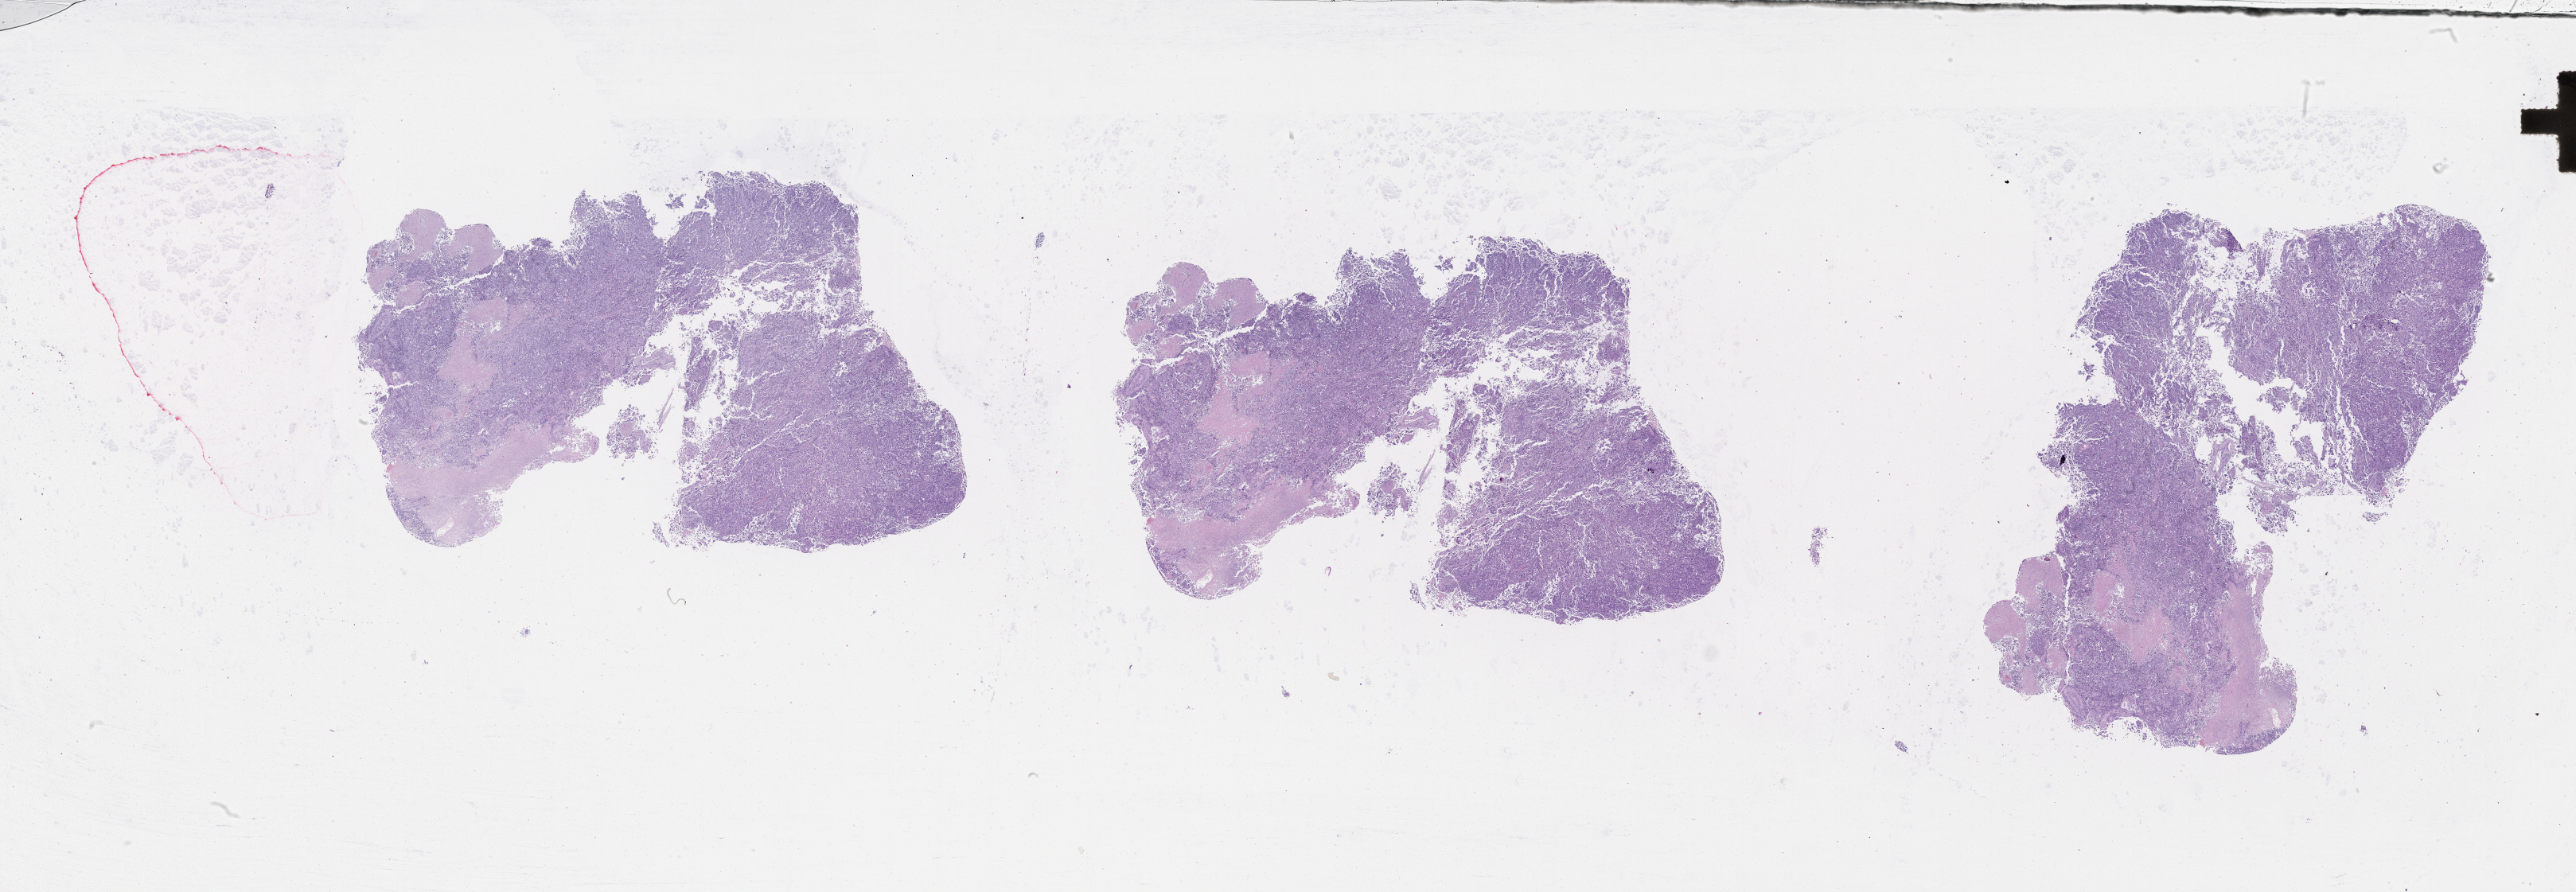
Whole-slide histology image, H&E, low-resolution overview of the scanned area, about 52.1 x 18.0 mm. Patient: female, age 62 years.
Patient diagnosis: Malignant melanoma, NOS.